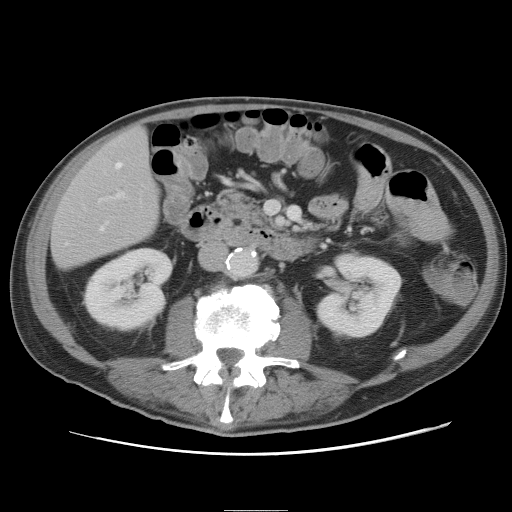
Contrast-enhanced abdominal CT, one axial slice; slice 18 of 89 in the series (ordered by position); 120 kVp; intravenous contrast given; soft-tissue window (W 400 / L 40 HU); 5 mm slice thickness; 512 × 512 image matrix, field of view 375 × 375 mm. Male patient, age 69 years. From the clinical record (not read from this slice): diagnosis: colorectal cancer liver metastases, imaged before liver resection; multiple liver metastases: no; largest metastasis: 8.5 cm; disease in both lobes: no.
Annotated regions visible in this slice (manually delineated by an expert):
- hepatic veins: box from (x=101, y=162) to (x=122, y=230) px
- liver: (x=52, y=127)–(x=159, y=269)
- planned liver remnant (the part of the liver to remain after resection): (x=53, y=126)–(x=159, y=269)
- portal vein (with intrahepatic branches): (x=117, y=191)–(x=125, y=198)